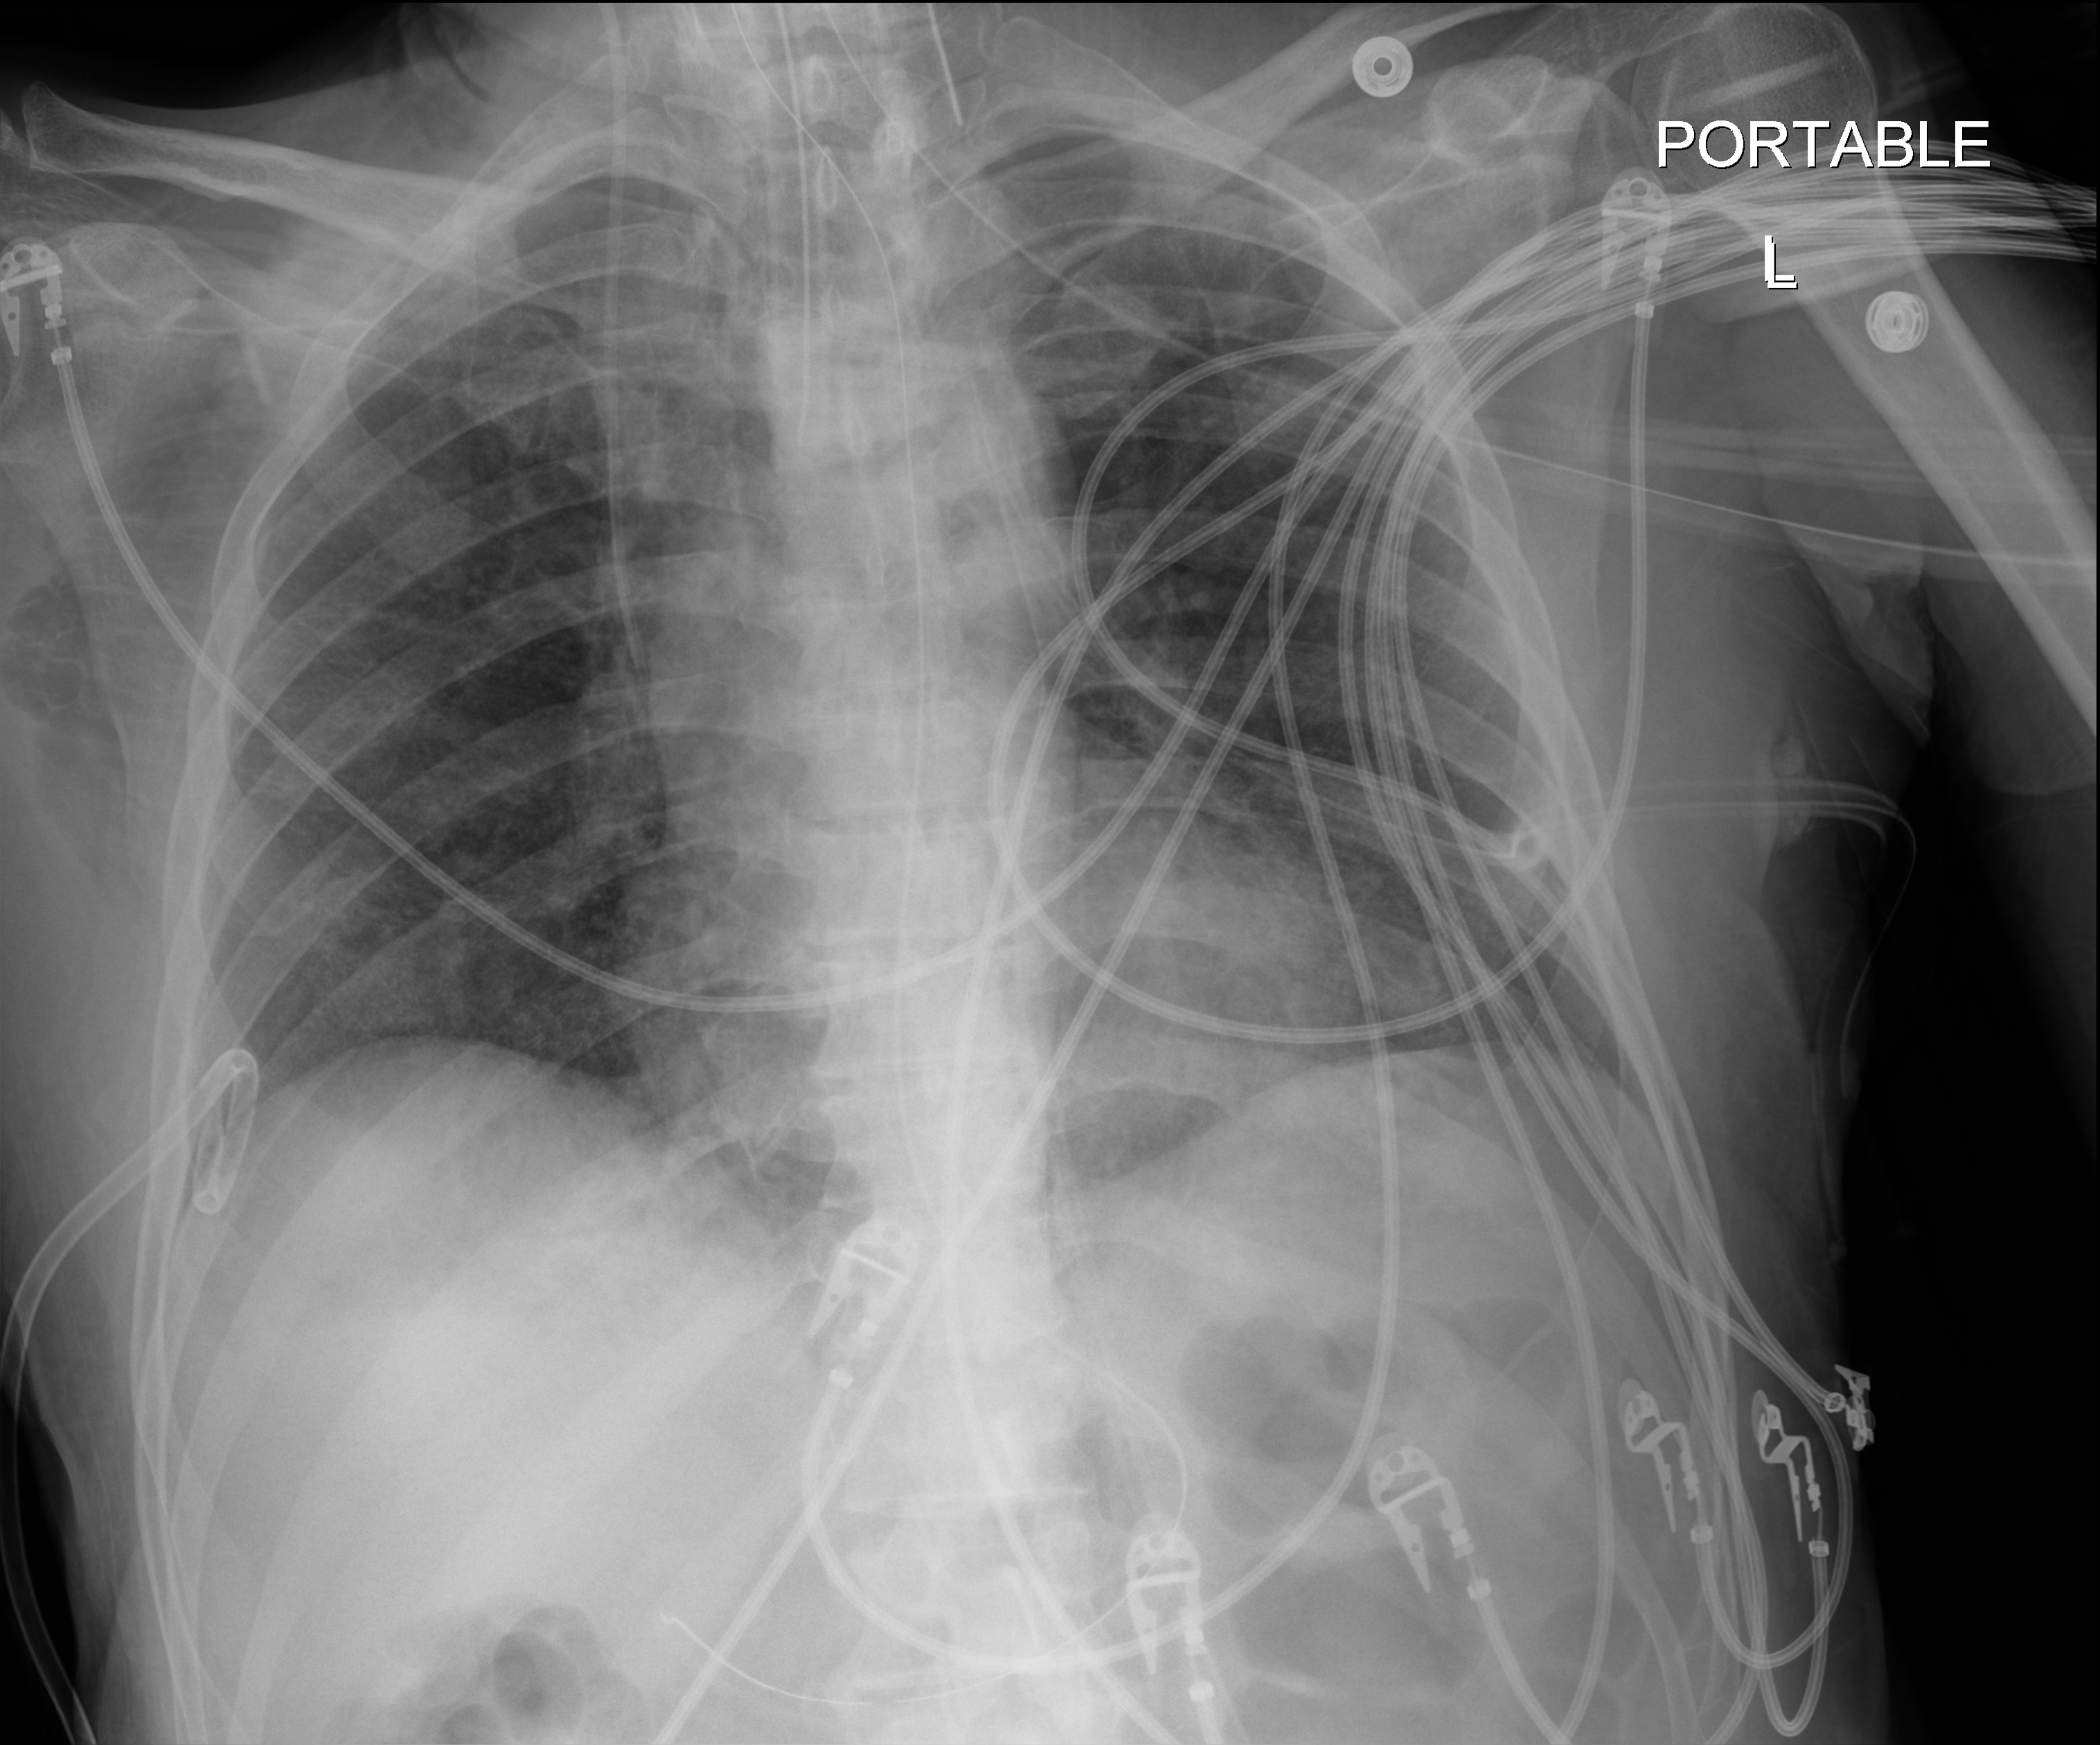
Chest X-ray (portable); anteroposterior (AP) projection. Patient hospitalised with COVID-19; male, aged 18–59 years.
From the hospital-stay record, not from the radiograph (when in the stay this image was taken is not recorded):
- mechanically ventilated during this hospital stay: yes
- length of hospital stay: 77 days
- admitted to intensive care during this hospital stay: yes